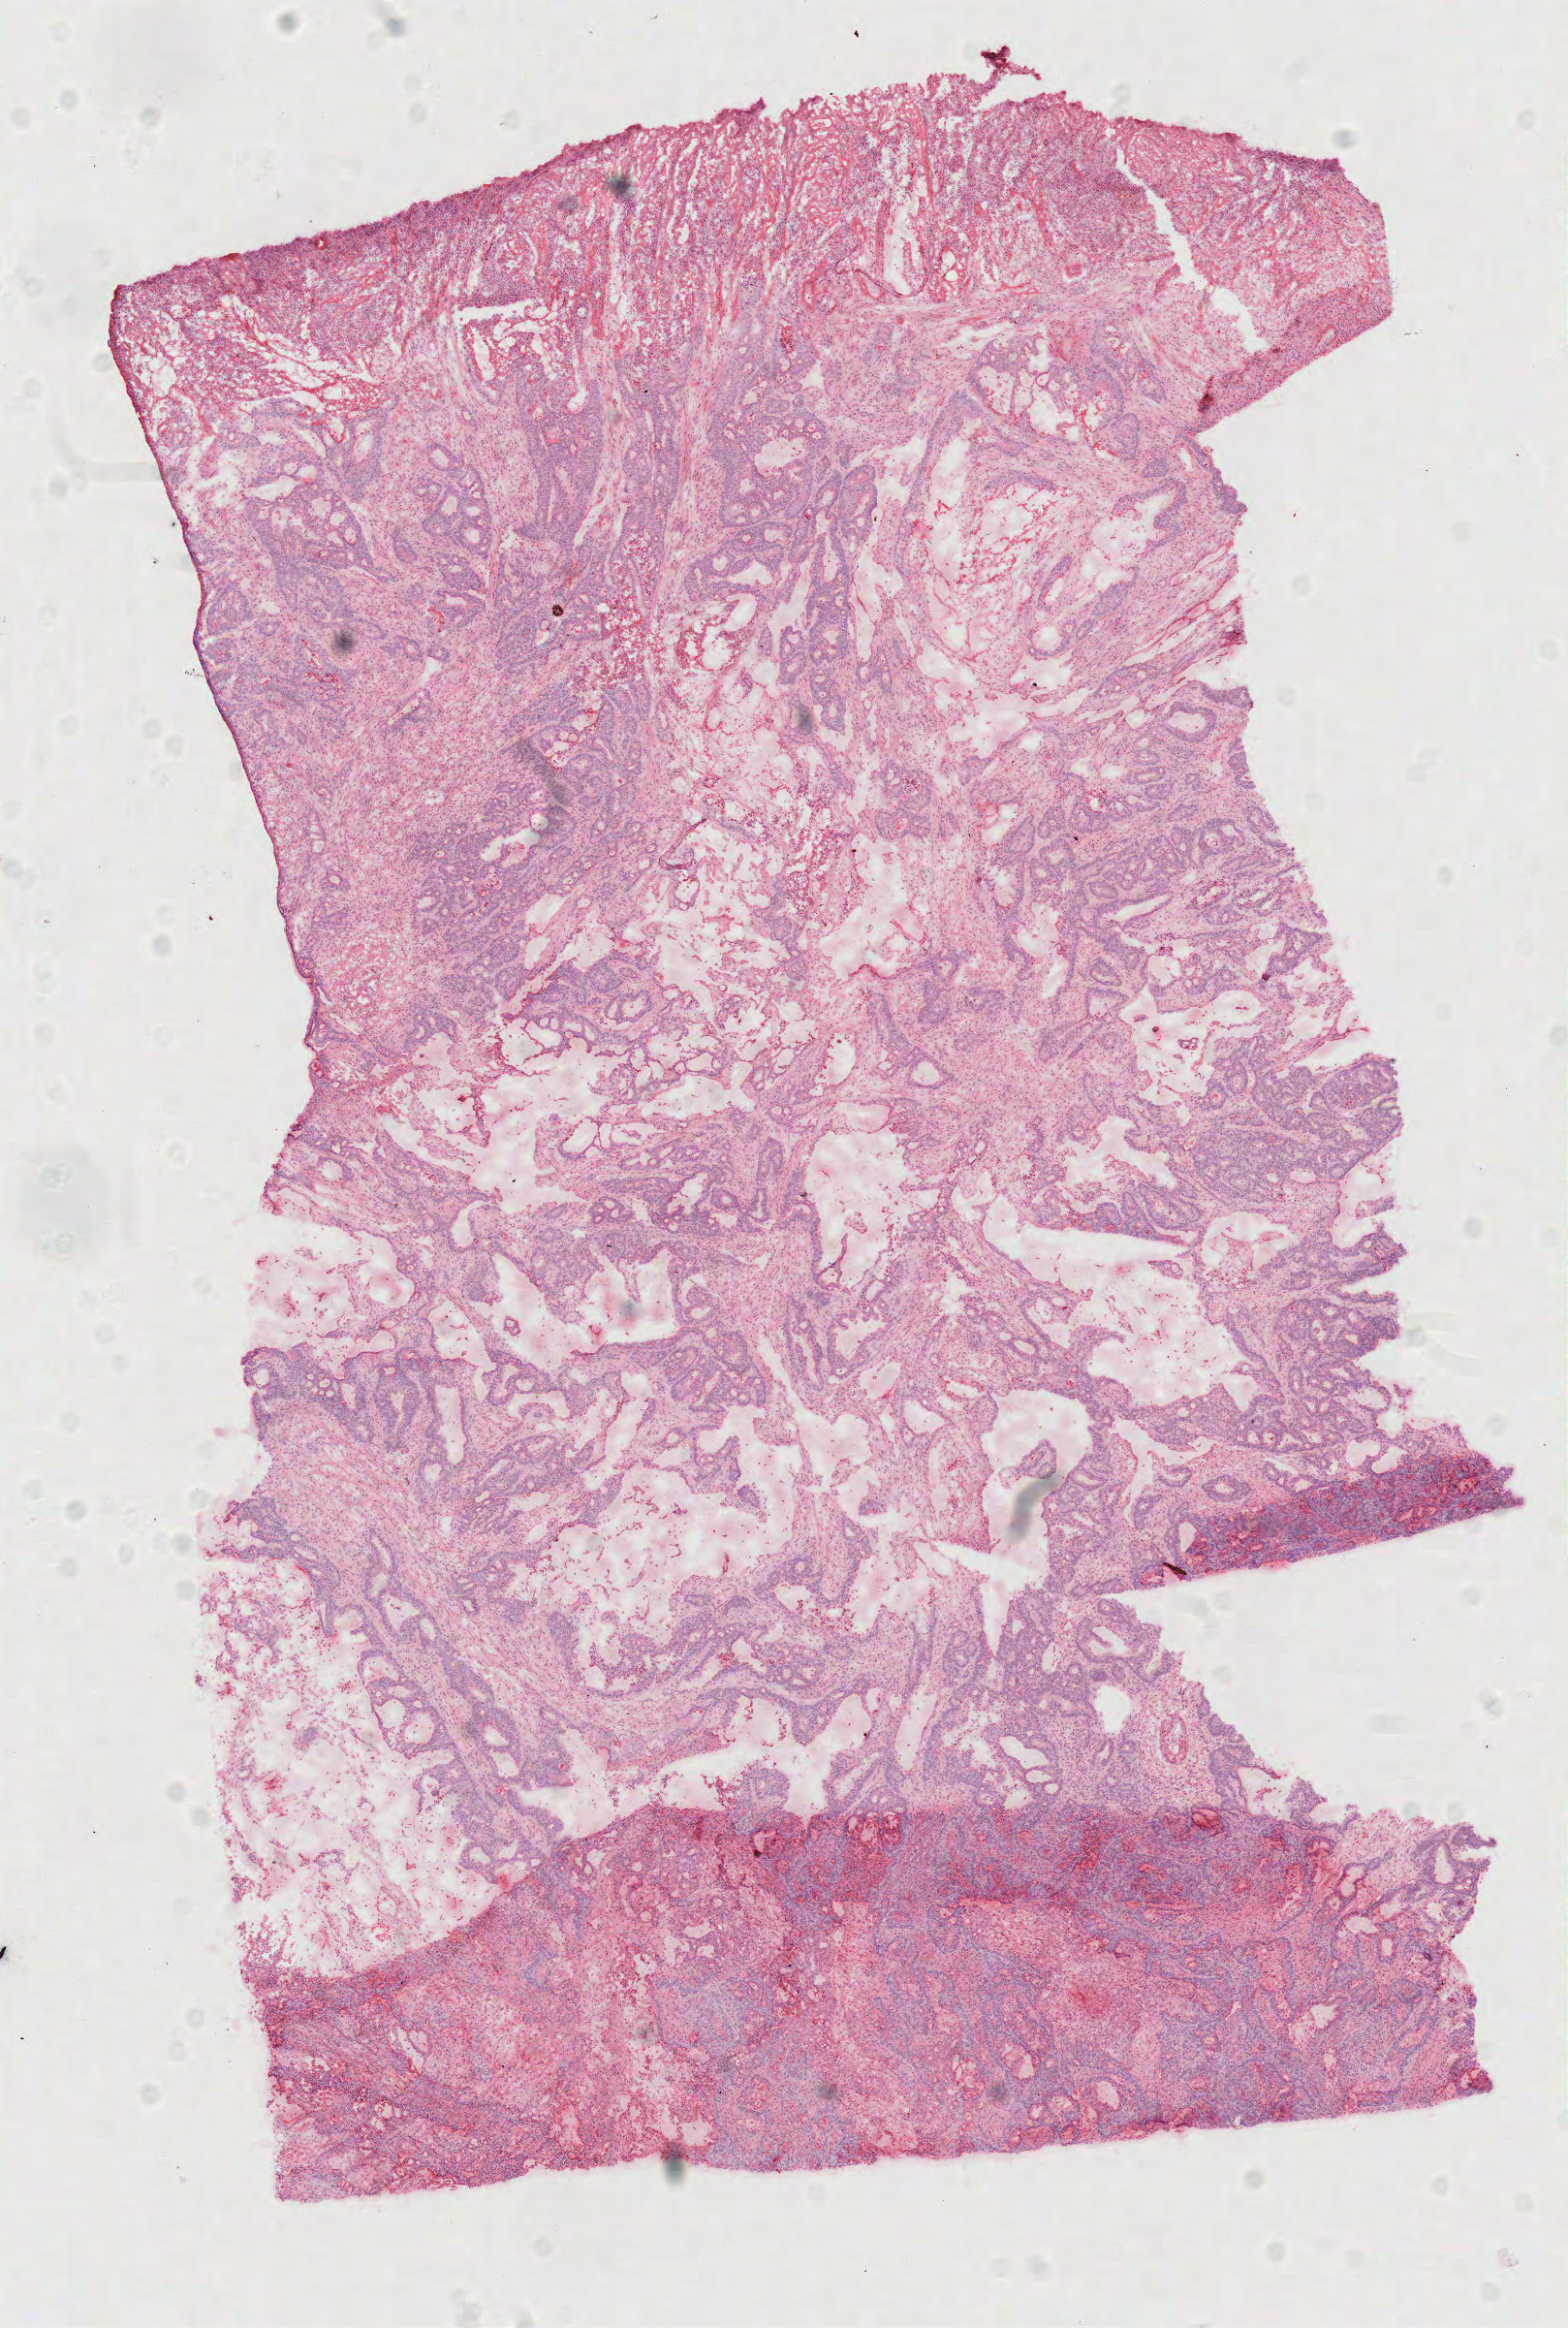
Hematoxylin and eosin (H&E) stained whole-slide image, low-resolution overview of the scanned area, about 6.4 x 9.4 mm (slide scanned at 40x). Frozen section from the top of the tissue portion. Primary tumour sample from the rectum. Patient: male, age at initial diagnosis 60 years. Slide review estimates, as recorded: tumour cells 70%, tumour nuclei 80%, normal cells 0%, stromal cells 20%, necrosis 10%.
• AJCC pathologic stage: IIA
• pathologic diagnosis: Mucinous adenocarcinoma